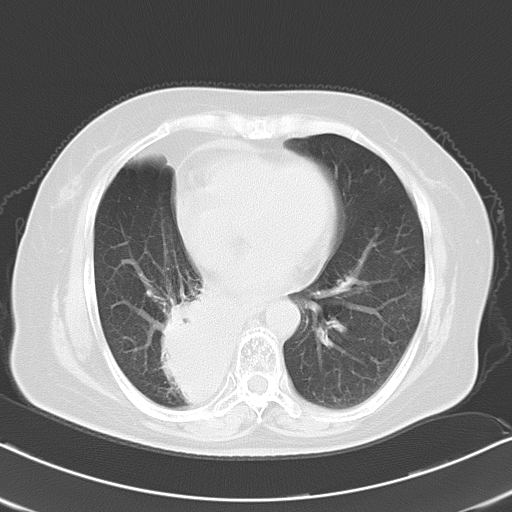
Chest CT, one axial slice. Slice 8 of 21 in the series (ordered by position). Reconstruction kernel B70f. 120 kVp. Lung window (W 1500 / L -600 HU). 512 × 512 image matrix, field of view 326 × 326 mm. Female patient, age 61 years. From the clinical record (not read from this slice): clinical TNM (as recorded): T1b N0 M1b.
Annotated regions visible in this slice (rectangle marked by the reading radiologist):
- lung tumour (recorded histology: squamous cell carcinoma): box from (x=150, y=278) to (x=236, y=423) px